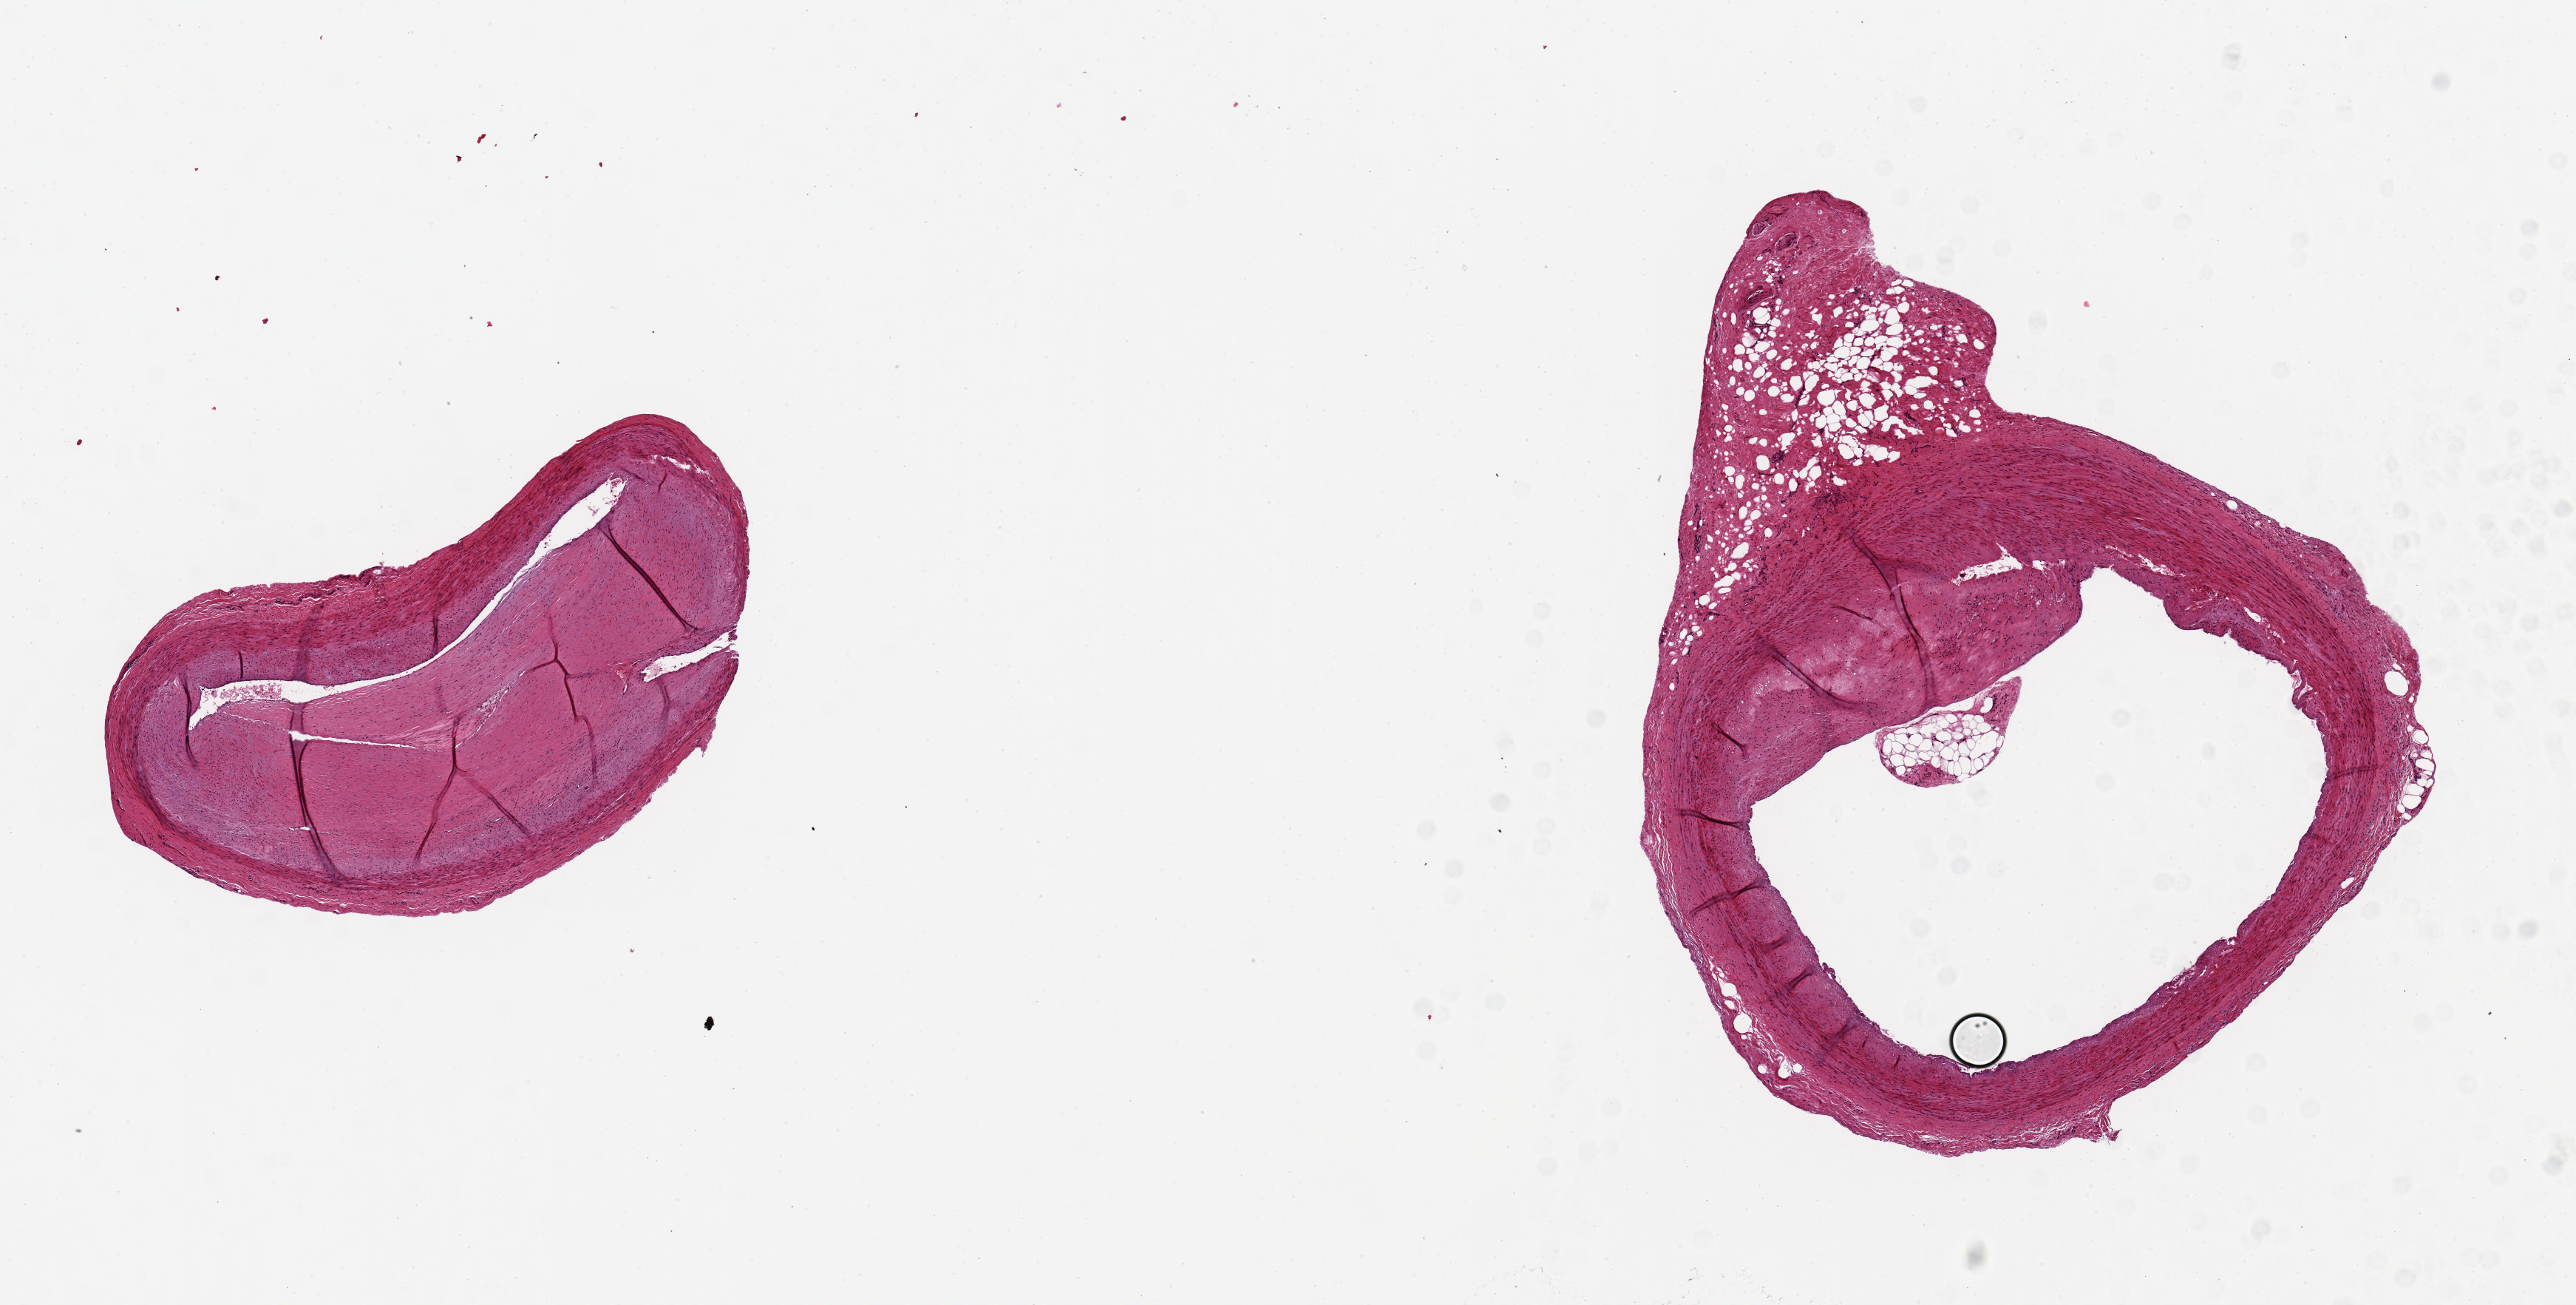
Whole-slide image, haematoxylin and eosin stain, shown as a low-resolution overview of the whole scanned area (about 13.8 x 7.0 mm, acquisition: 20x scan), PAXgene-fixed, paraffin-embedded tissue, target tissue: coronary artery, donor tissue sample.
Pathologist's review note for this sample: 2 pieces, 4x2 & 5x4mm; one with nearly total atherosclerotic occlusion, the other with ~30% occlusion.